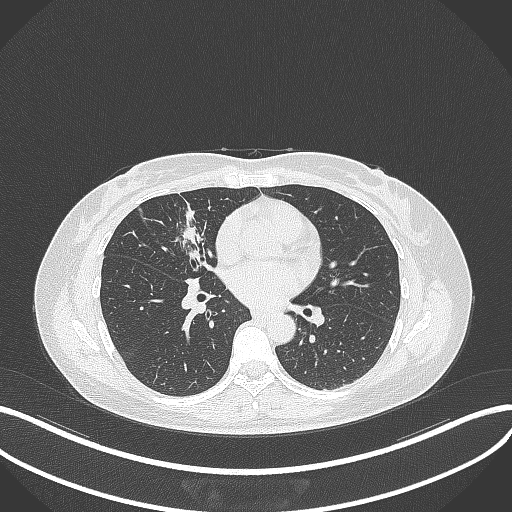
Chest CT, one axial slice; slice 143 of 284 in the series (ordered by position); reconstruction kernel B70f; lung window (W 1500 / L -600 HU); 512 × 512 image matrix. Patient: female, 43 years. From the clinical record (not read from this slice): clinical TNM (as recorded): T1c N3 M1.
Structures marked on this image (rectangle marked by the reading radiologist):
- lung tumour (recorded histology: adenocarcinoma): bounding box [x1, y1, x2, y2] px = [173, 208, 205, 246]